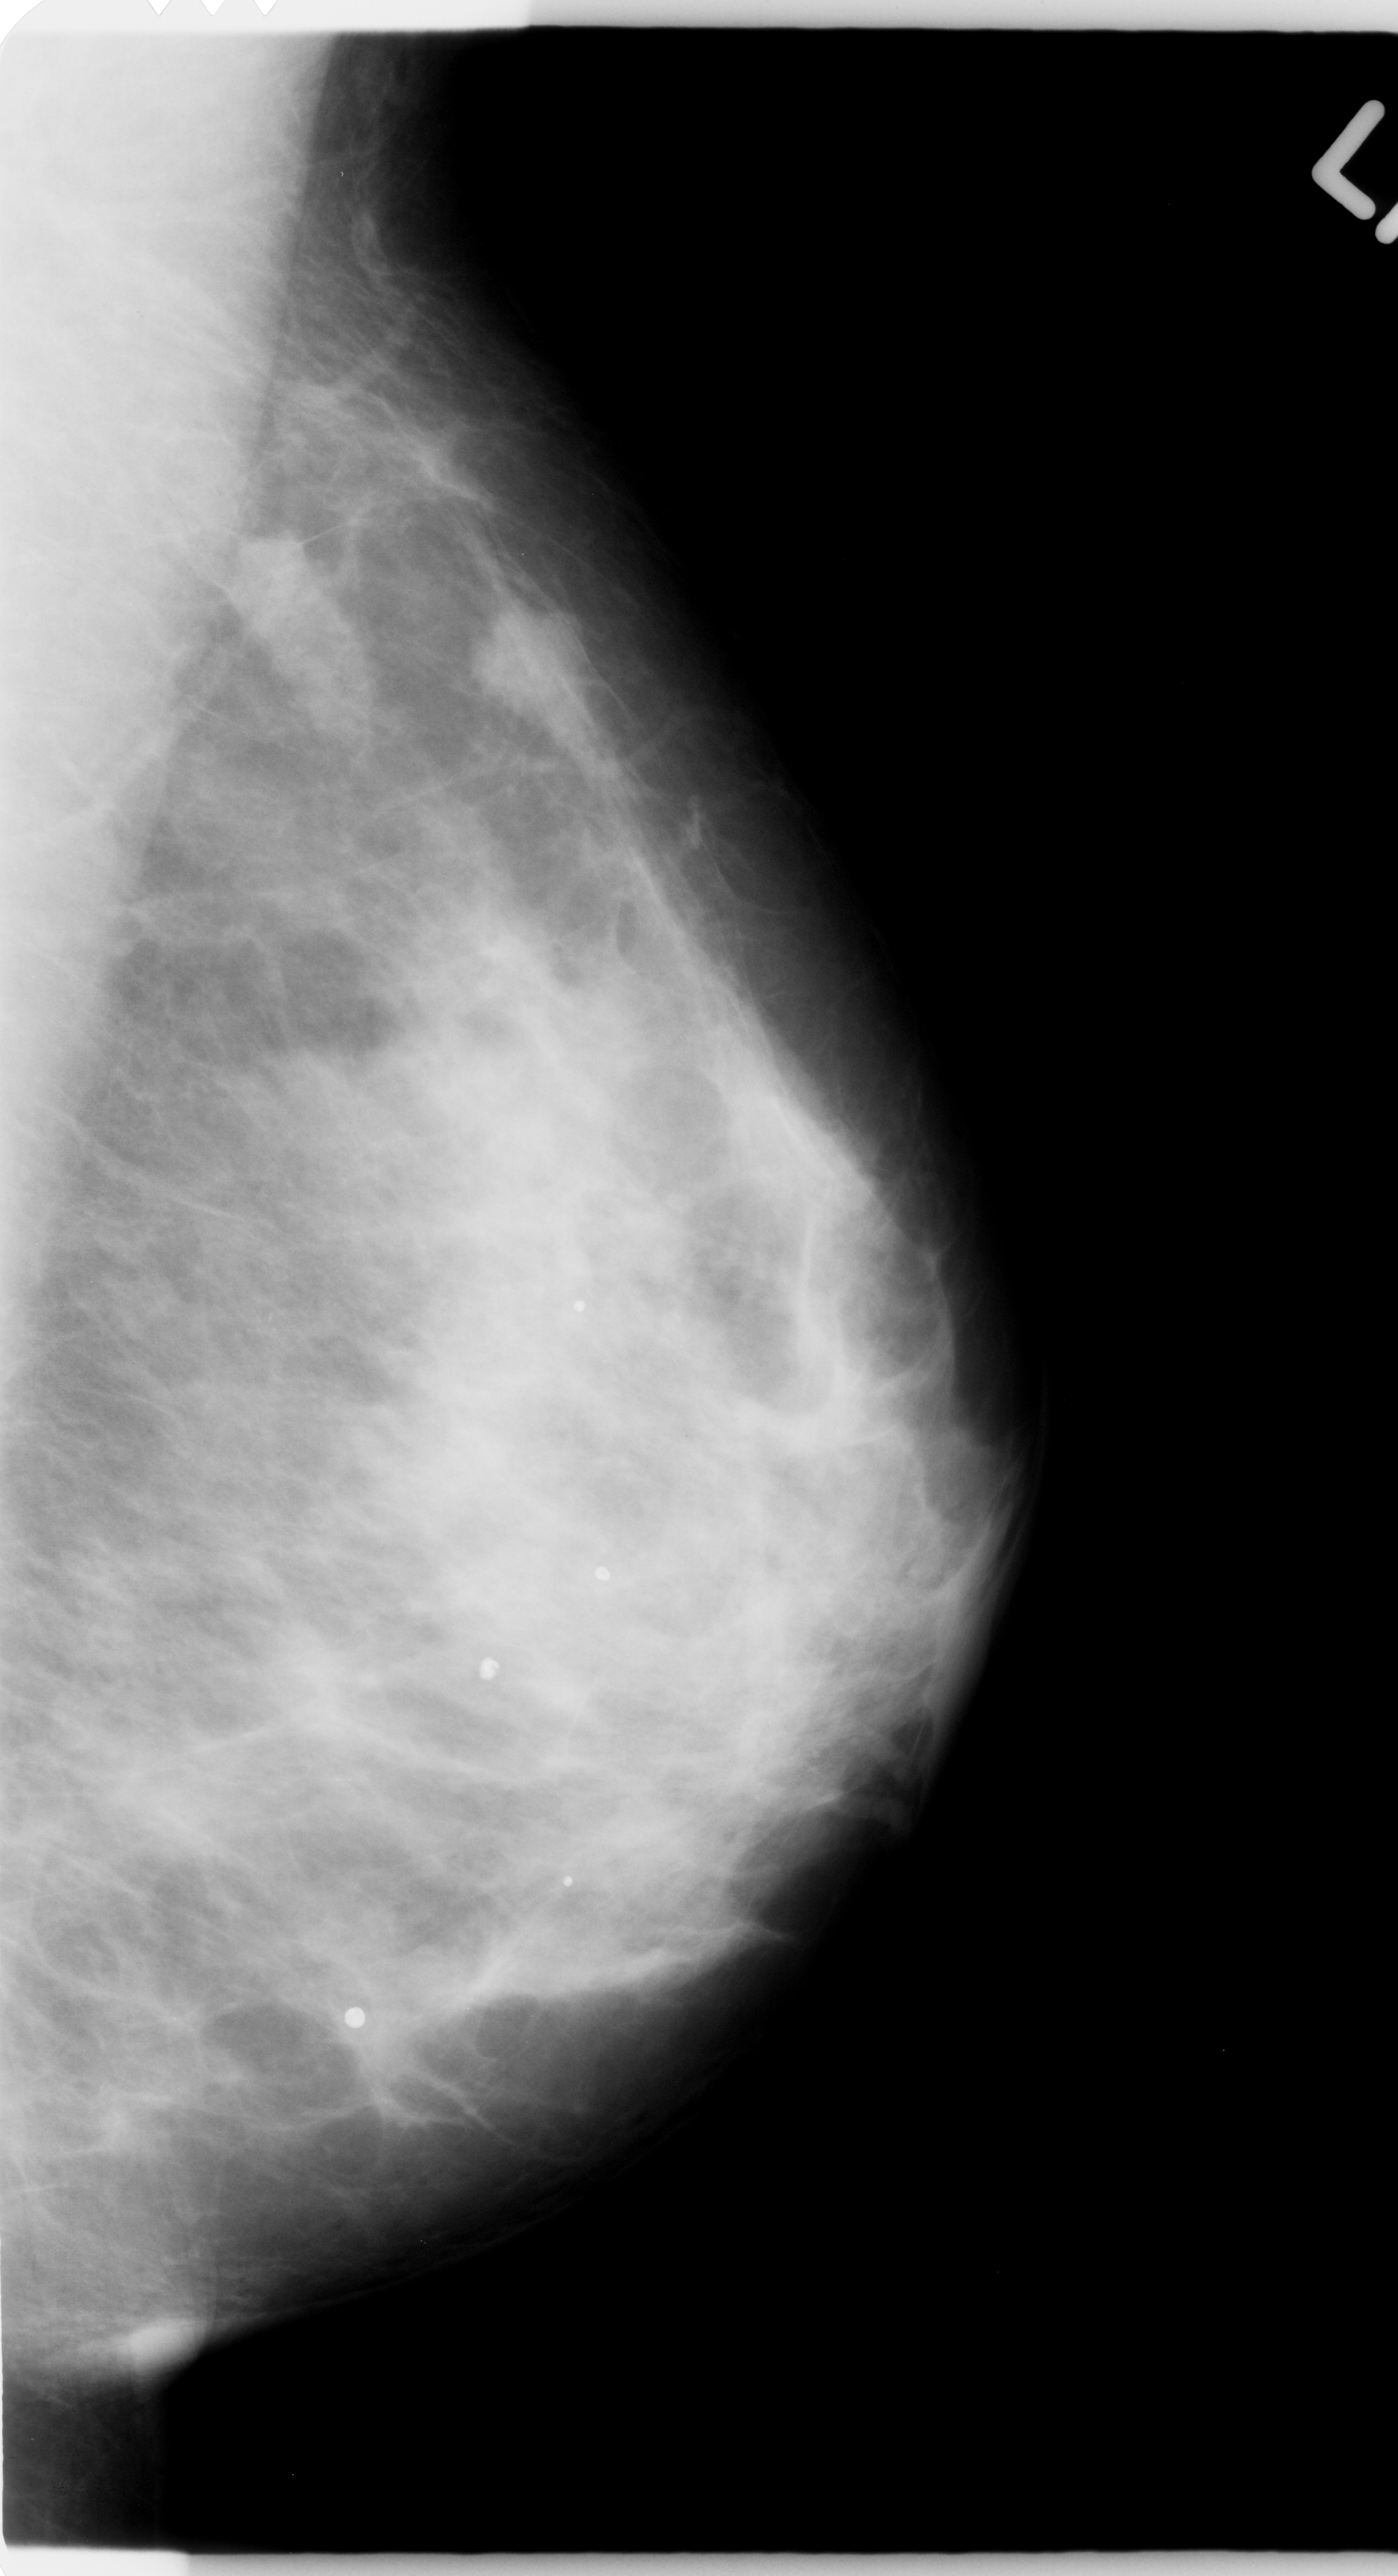
Mammogram (digitized film). Left breast. Mediolateral oblique (MLO) view. Breast composition: heterogeneously dense (BI-RADS density category 3 of 4). 1398 × 2576 image matrix.
Expert-marked regions of interest on this image (one box per marked abnormality):
- mass, shape lobulated, margins microlobulated; BI-RADS assessment category 4; pathology result (as recorded, not read from the image): malignant: bounding box [x1, y1, x2, y2] px = [449, 581, 621, 760]